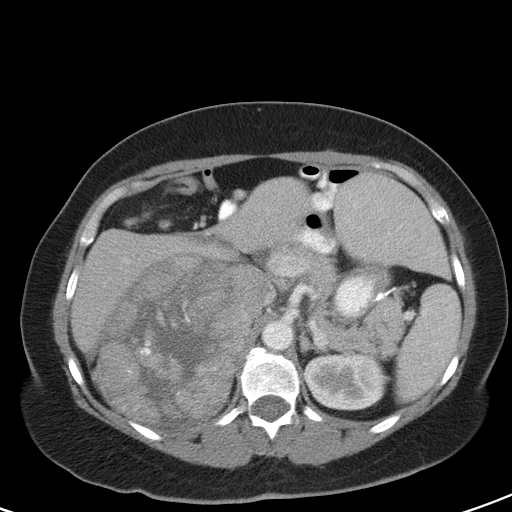
Contrast-enhanced abdominal CT, one axial slice; slice 71 of 126 in the series (ordered by position); 120 kVp; soft-tissue window (W 400 / L 40 HU); 5 mm slice thickness; 512 × 512 image matrix, field of view 356 × 356 mm. Patient: female, 51 years. Case-level facts recorded for this patient, not image findings: diagnosis: adrenocortical carcinoma; tumour side: right adrenal; tumour size at pathology: 17 cm; Ki-67 index: 12 %; stage (as recorded): 2.
Outlined on this slice (semi-automatic segmentation, software-assisted and operator-edited):
- mass: bounding box (x1, y1, x2, y2) in pixels: (98, 256, 262, 422)